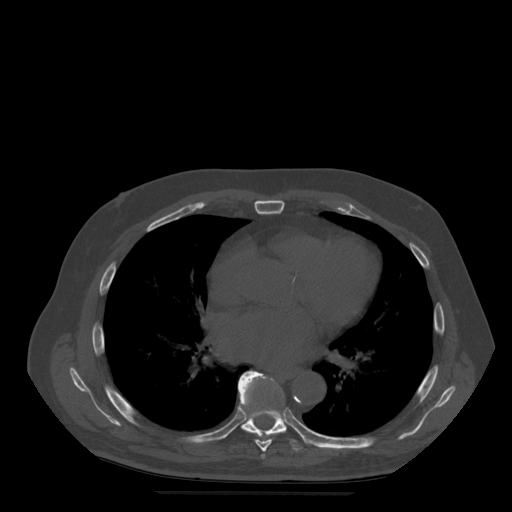
CT including the spine, one axial slice. Position 323 of 522 along the scan axis. Bone window (W 1800 / L 400 HU). 512 × 512 image matrix, field of view 420 × 420 mm. Patient age 72 years. Case-level facts recorded for this patient, not image findings: primary cancer: prostate.
Outlined on this slice (semi-automatically segmented with operator editing):
- T6 vertebra: bounding box <262,455,265,459> (left, top, right, bottom; pixels)
- T7 vertebra: <238,373,273,452>
- T8 vertebra: <238,371,310,451>